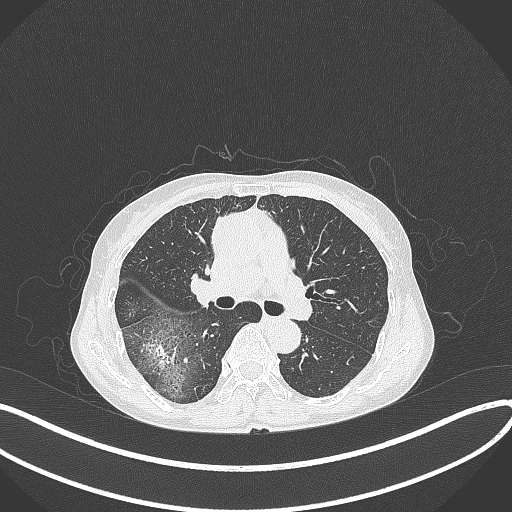
Chest CT, one axial slice. Position 238 of 371 along the scan axis. Reconstruction kernel B70f. 120 kVp. Lung window (W 1500 / L -600 HU). 1 mm slice thickness. 512 × 512 image matrix, field of view 400 × 400 mm. Female patient, age 69 years. Case-level facts recorded for this patient, not image findings: clinical TNM (as recorded): T1b N0 M0; histopathological grade: G2-3.
Structures marked on this image (rectangle marked by the reading radiologist):
- lung tumour (recorded histology: adenocarcinoma): bounding box [x1, y1, x2, y2] px = [144, 335, 180, 374]